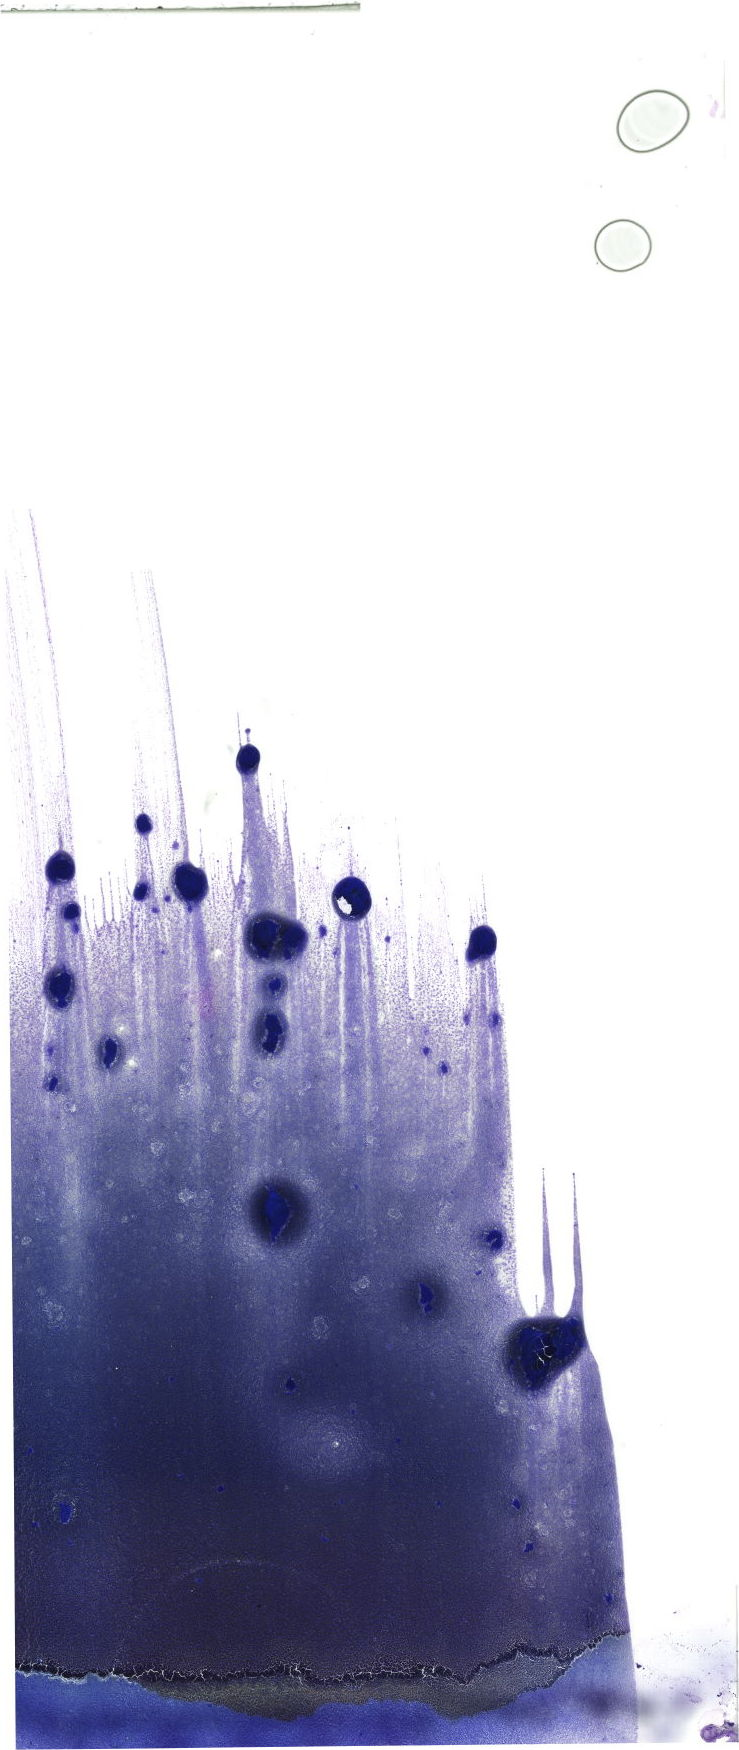
Whole-slide image of a May-Grünwald–Giemsa-stained bone marrow aspirate smear — a low-resolution overview of the entire scanned area, about 20.9 x 49.6 mm. Patient sex: male.
Diagnosis: Chronic Phase Chronic Myeloid Leukemia, BCR-ABL1 Positive.